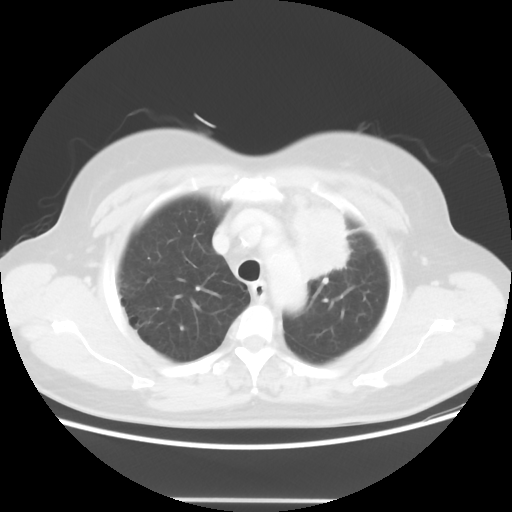
Chest CT, one axial slice; position 43 of 52 along the scan axis; reconstruction kernel STANDARD; lung window (W 1500 / L -600 HU); 512 × 512 image matrix. Female patient, age 52 years. Case-level facts recorded for this patient, not image findings: clinical TNM (as recorded): T2 N3 M0.
Outlined on this slice (rectangle marked by the reading radiologist):
- lung tumour (recorded histology: adenocarcinoma): box from (x=289, y=185) to (x=360, y=284) px